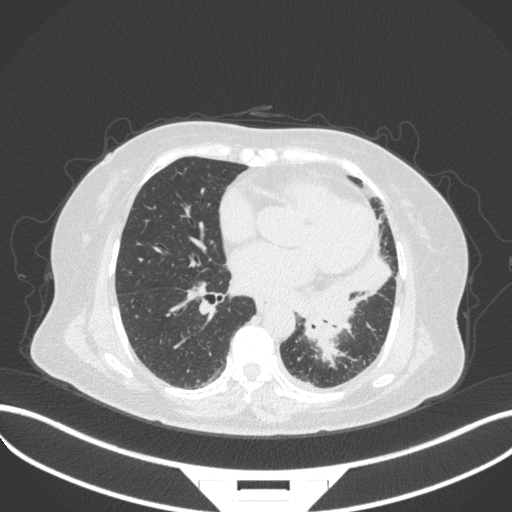
Chest CT, one axial slice. Position 155 of 328 along the scan axis. Reconstruction kernel B31f. 120 kVp. Lung window (W 1500 / L -600 HU). 512 × 512 image matrix, field of view 400 × 400 mm. Female patient, age 69 years. From the clinical record (not read from this slice): clinical TNM (as recorded): T2b N3 M1.
Annotated regions visible in this slice (bounding box drawn by a radiologist):
- lung tumour (recorded histology: adenocarcinoma): bounding box <298,275,358,356> (left, top, right, bottom; pixels)